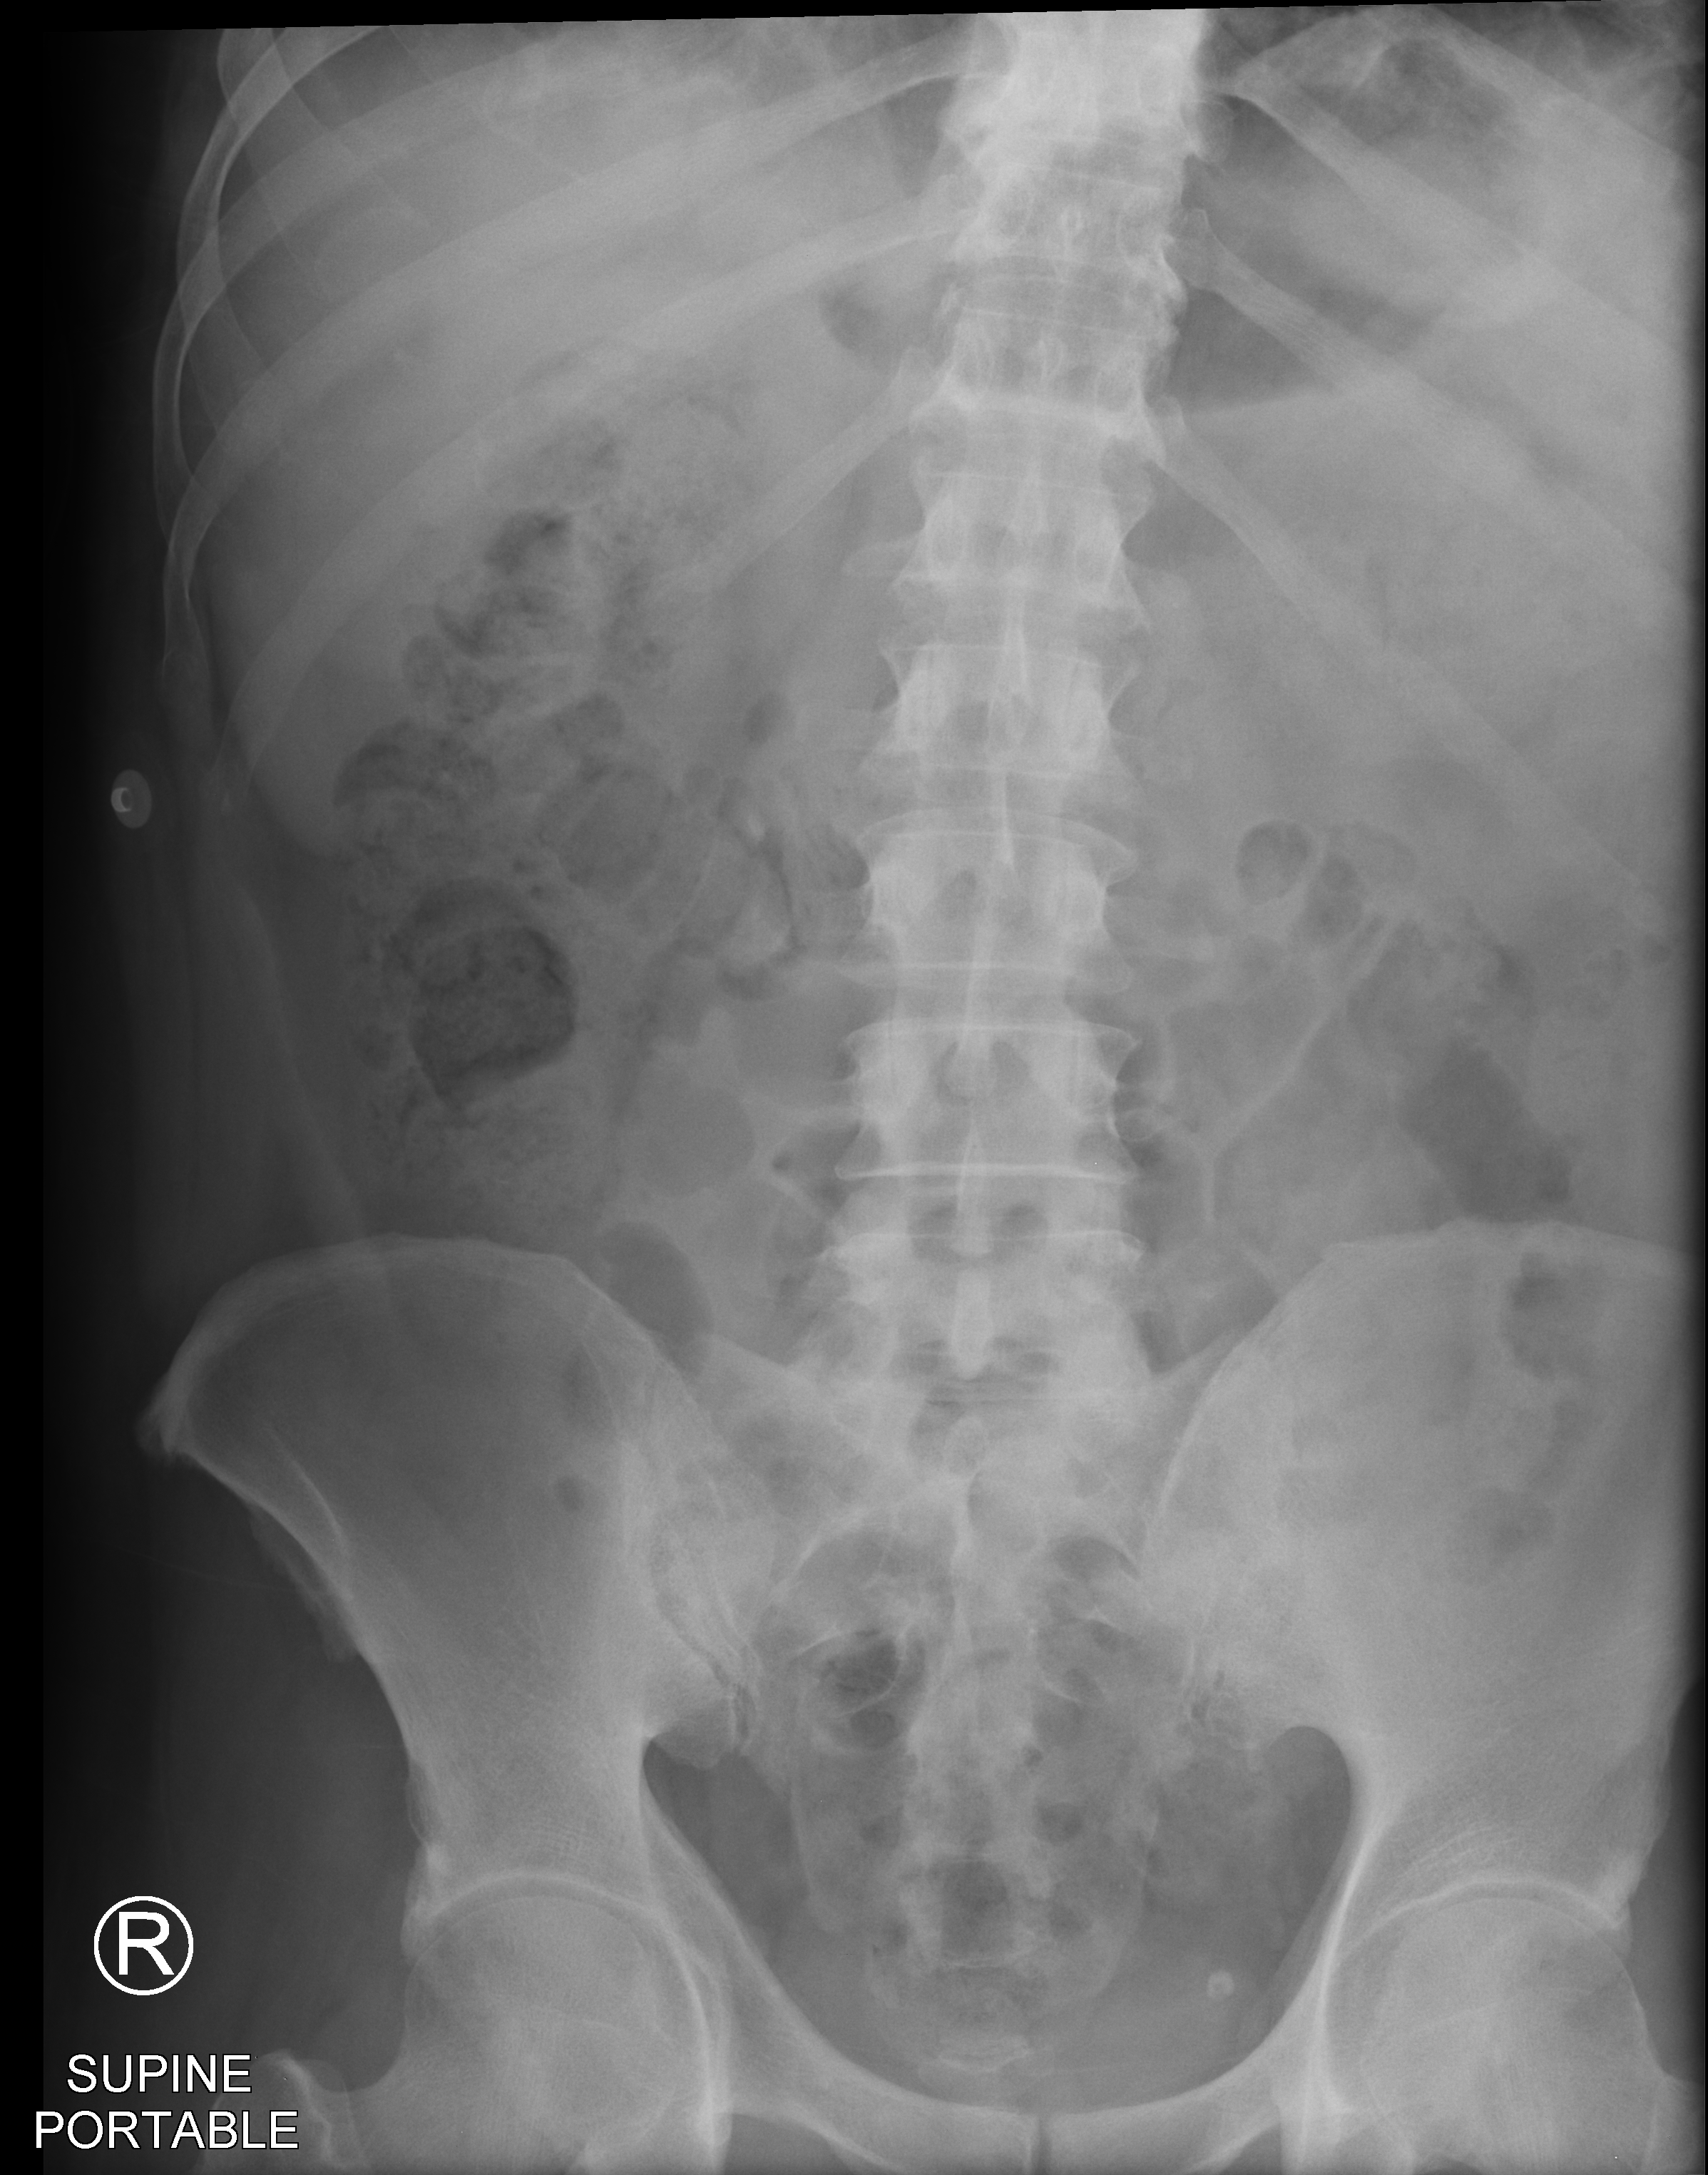
Bedside abdomen radiograph (computed radiography), anteroposterior (AP) projection. Male patient hospitalised with COVID-19, age 18–59 years.
Admission-level facts for this patient (not findings on this image; timing relative to this image not recorded): mechanically ventilated during this hospital stay: no; diabetes (admission record): no; admitted to intensive care during this hospital stay: yes.